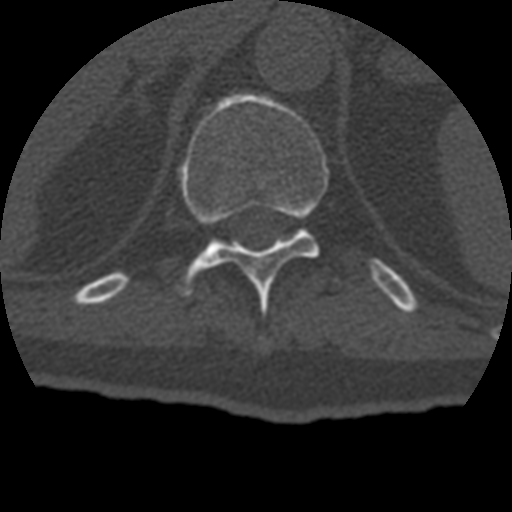
CT including the spine, one axial slice. Slice 194 of 399 in the series (ordered by position). 120 kVp. Bone window (W 1800 / L 400 HU). 1.25 mm slice thickness. 512 × 512 image matrix, field of view 160 × 160 mm. Patient age 69 years. From the clinical record (not read from this slice): primary cancer: prostate.
Annotated regions visible in this slice (semi-automatically segmented with operator editing):
- T11 vertebra: bounding box <179,93,330,296> (left, top, right, bottom; pixels)